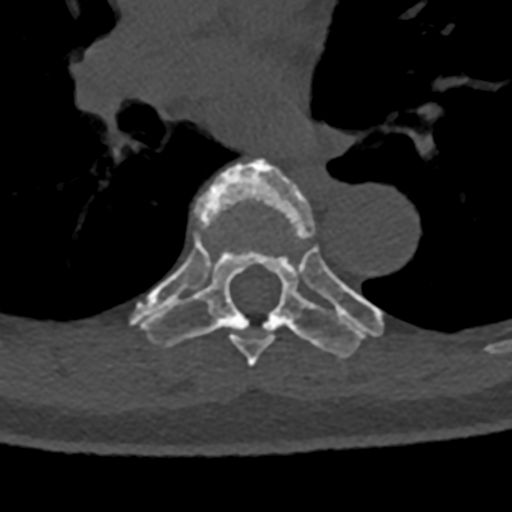
CT including the spine, one axial slice; position 780 of 797 along the scan axis; 120 kVp; bone window (W 1800 / L 400 HU); 0.5 mm slice thickness; 512 × 512 image matrix. Male patient, age 74 years. Case-level facts recorded for this patient, not image findings: primary cancer: renal.
Outlined on this slice (semi-automatic segmentation, software-assisted and operator-edited):
- T6 vertebra: bounding box <174,159,315,367> (left, top, right, bottom; pixels)
- T7 vertebra: <130,220,383,359>